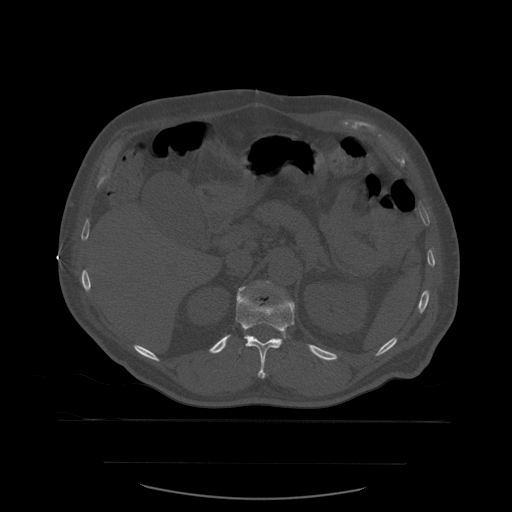
CT including the spine, one axial slice. Slice 268 of 590 in the series (ordered by position). Bone window (W 1800 / L 400 HU). 512 × 512 image matrix, field of view 479 × 479 mm. Patient age 71 years. Case-level facts recorded for this patient, not image findings: primary cancer: lung; vertebrae with lytic lesions (as recorded): T1, T2, L5, S1.
Annotated regions visible in this slice (semi-automatically segmented with operator editing):
- L1 vertebra: box from (x=258, y=281) to (x=295, y=305) px
- T12 vertebra: (x=236, y=287)–(x=295, y=379)